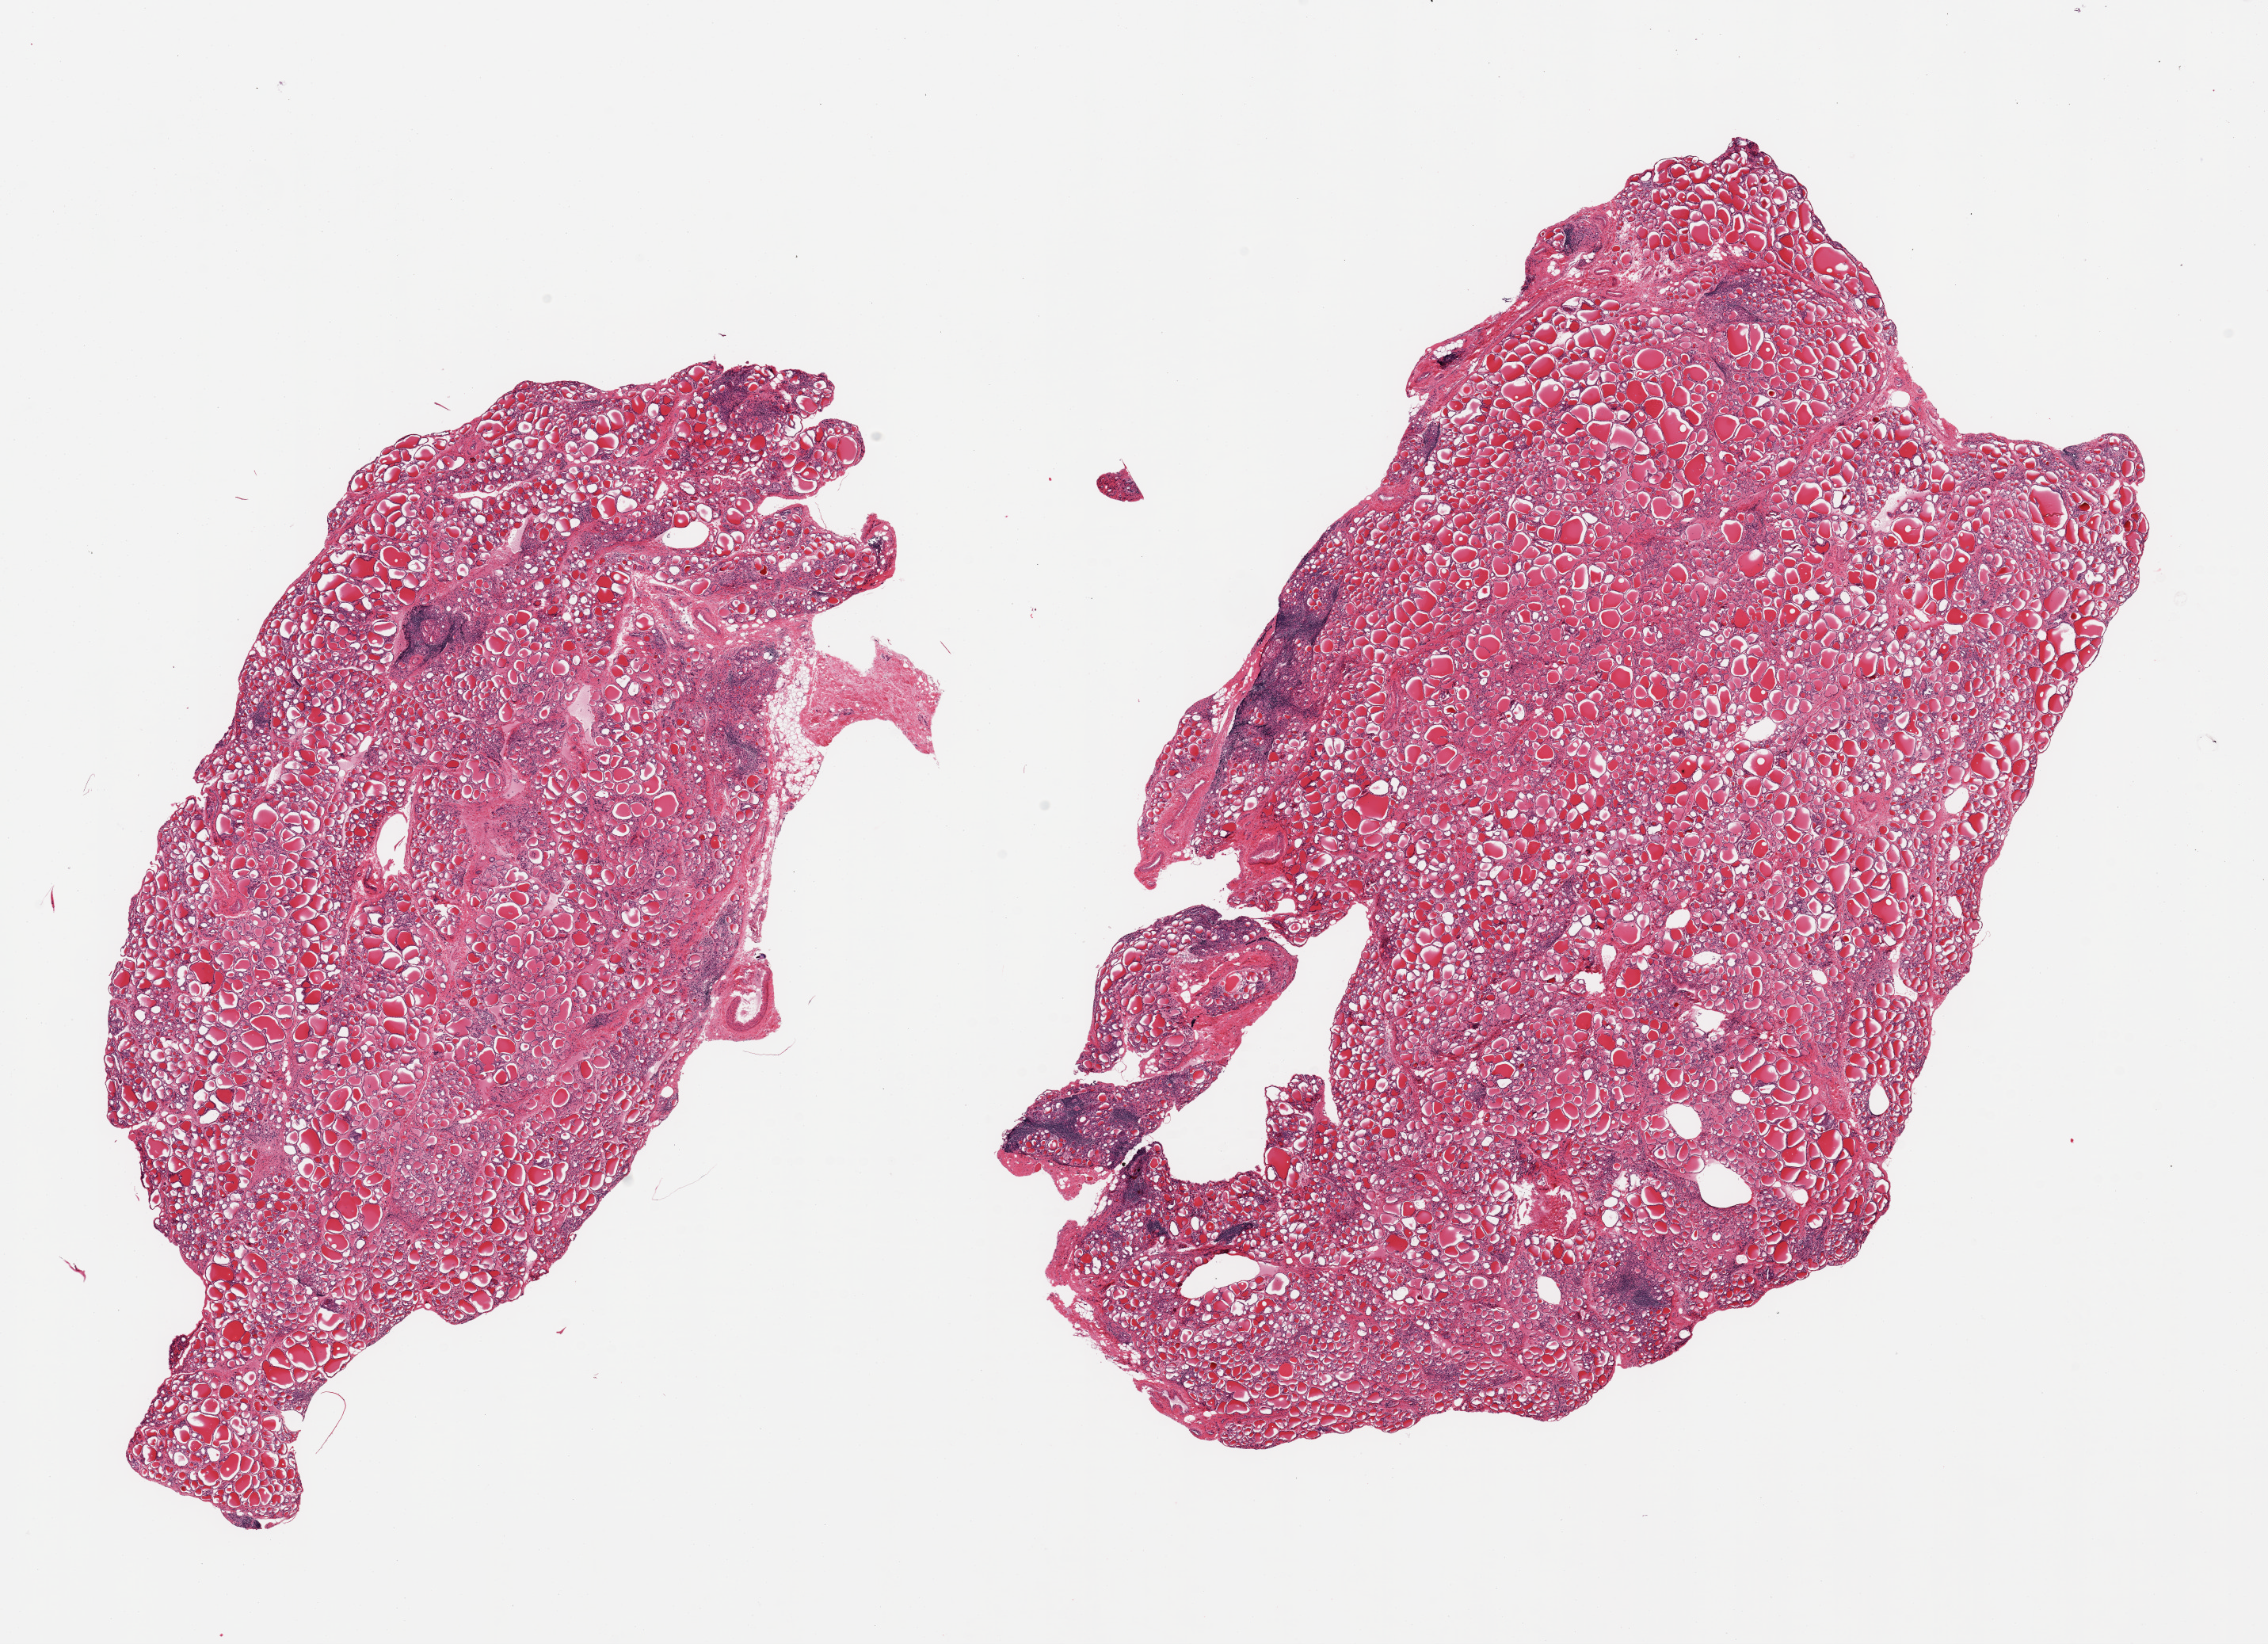
Digitized haematoxylin and eosin-stained section — shown as a low-resolution overview of the whole scanned area (about 22.6 x 16.4 mm, slide scanned at 20x); PAXgene-fixed, paraffin-embedded tissue; section of thyroid (target tissue); donor tissue sample. Donor sex: female.
Review note (as recorded): 2 pieces; mild interstitial fibrosis and aggregates of lymphocytes consistent with Hashimoto's (lymphocytic) thyroiditis.